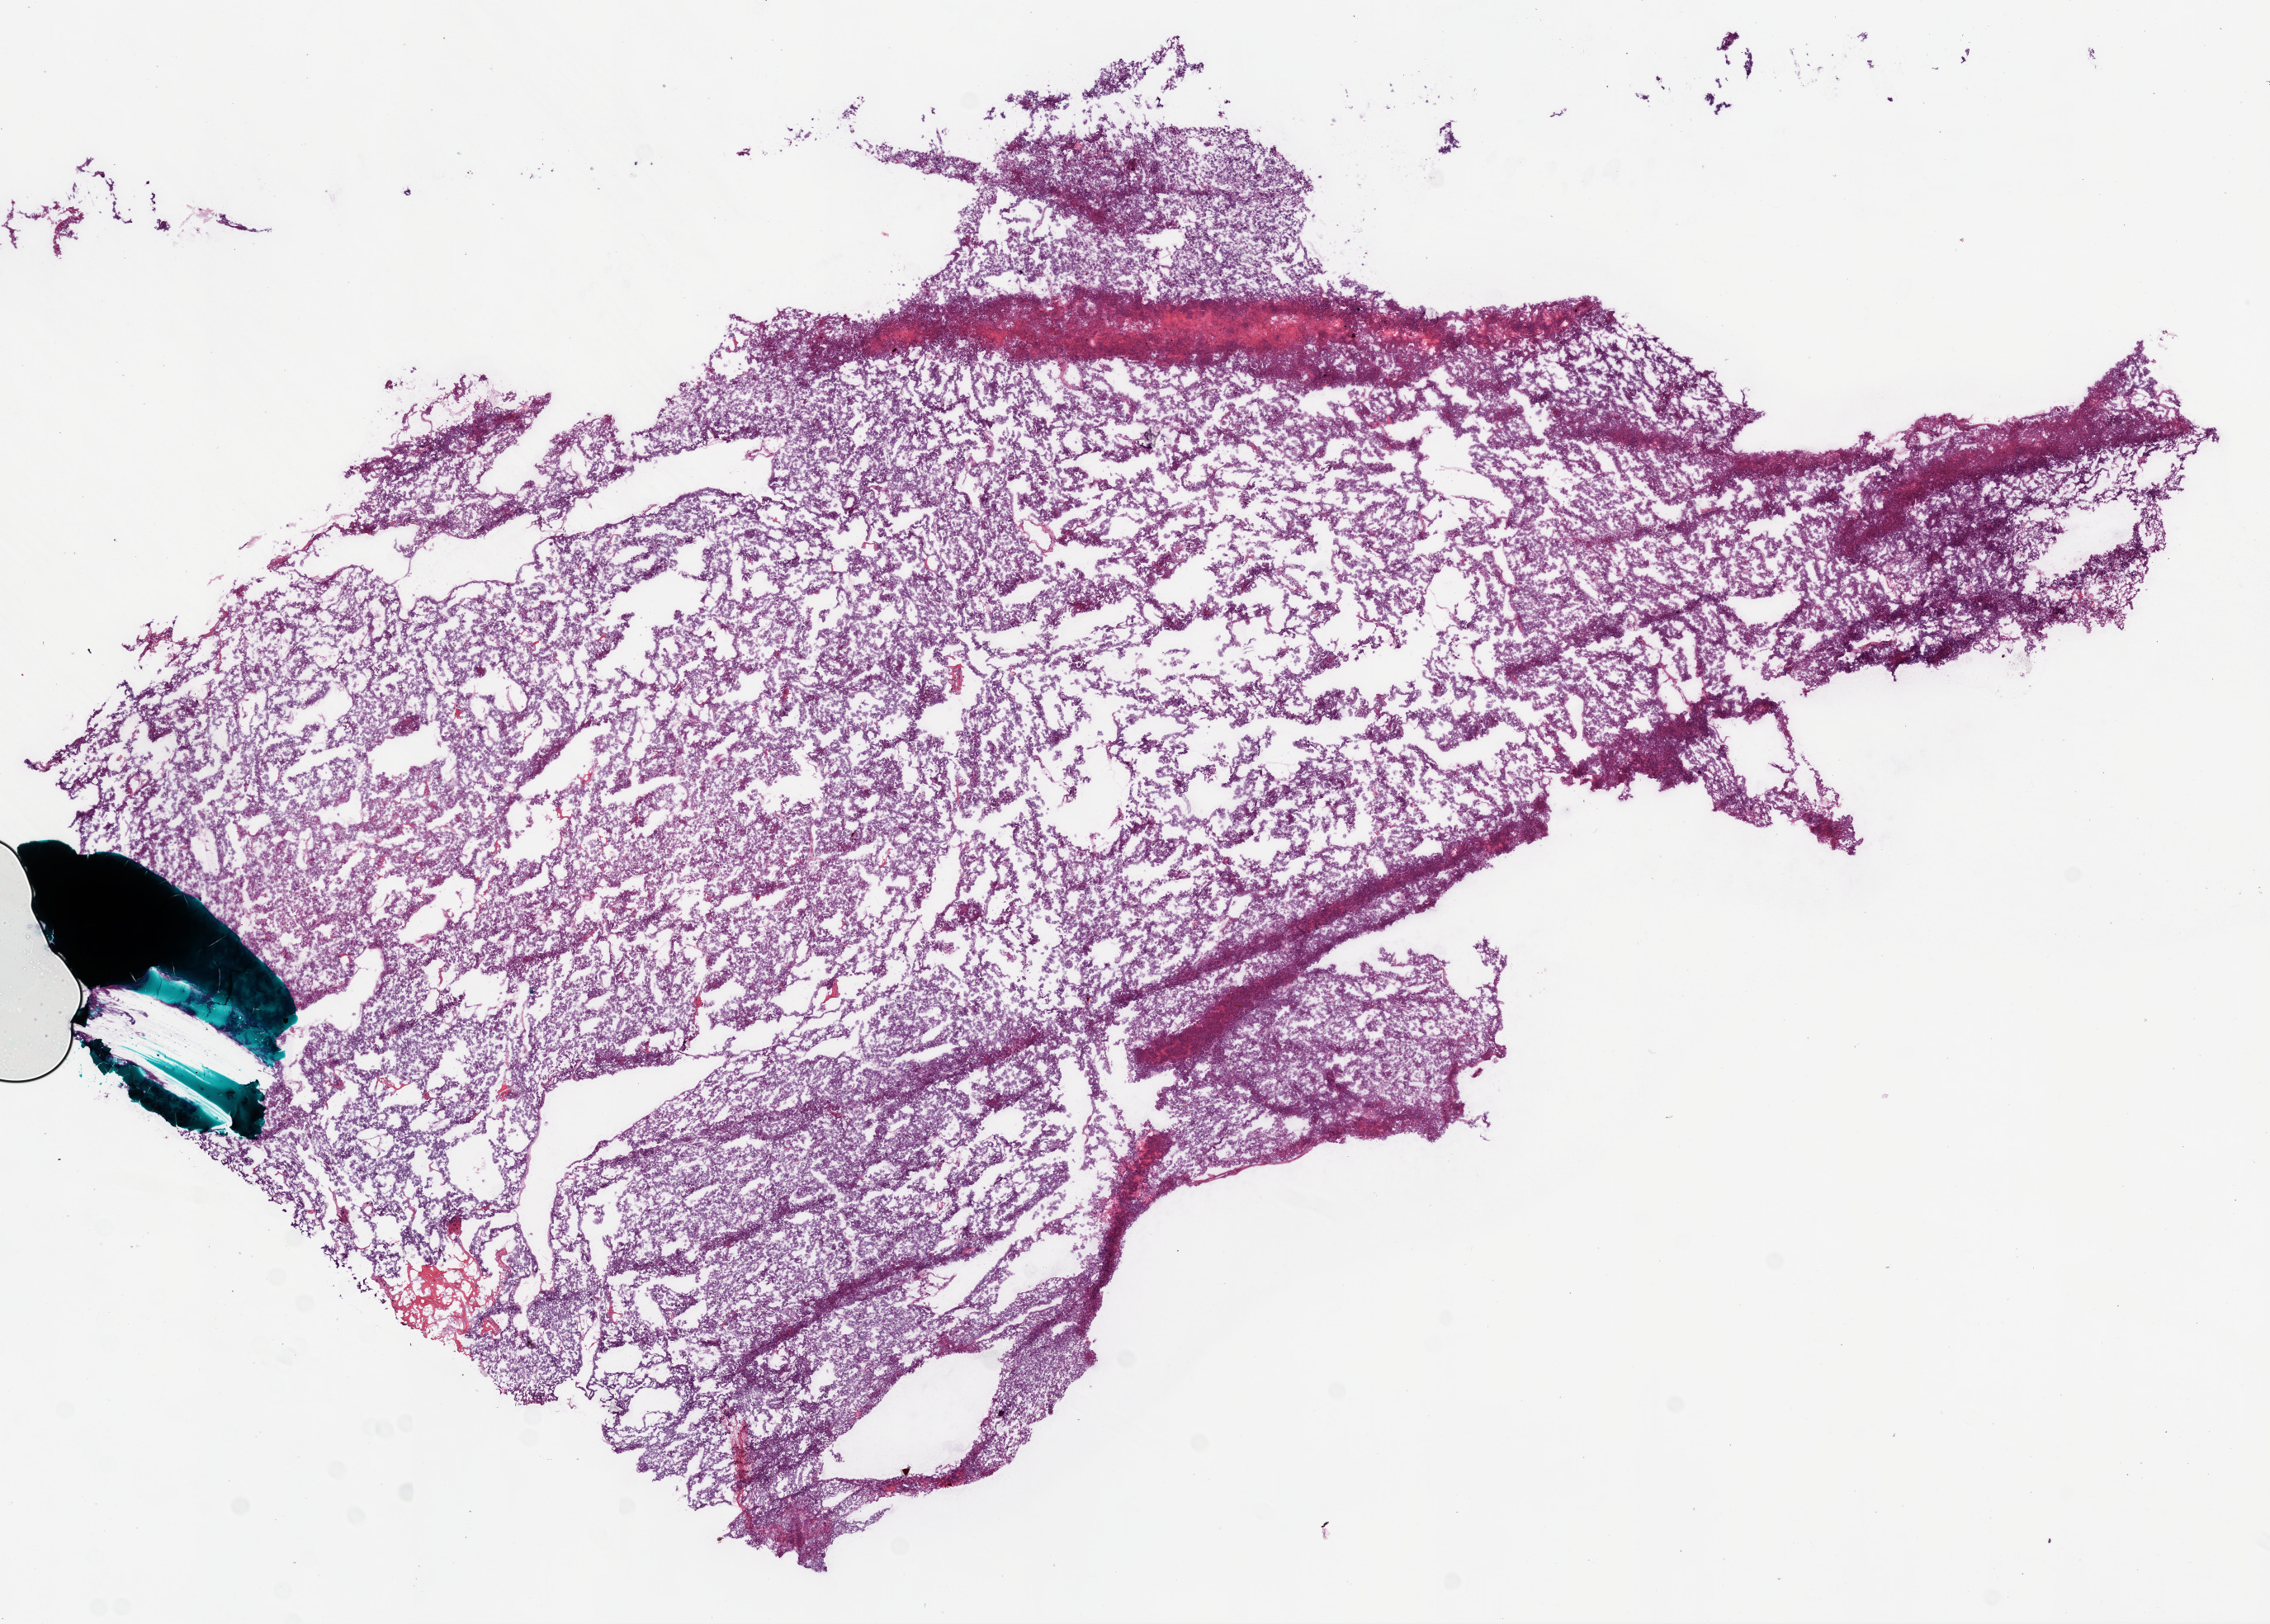
Whole-slide histology image, Hematoxylin and eosin (H&E) stained, shown as a low-resolution overview of the whole scanned area (about 11.0 x 7.9 mm), frozen section from the bottom of the tissue portion, primary tumour sample from the ovary. Female patient; age at initial diagnosis 57 years. Histologic grade: G3 (poorly differentiated). Composition of this section per pathologist review: tumour cells 98%, tumour nuclei 99%, normal cells 0%, stromal cells 1%, necrosis 1%.
FIGO stage: IIIC. Diagnosis: Serous cystadenocarcinoma, NOS.